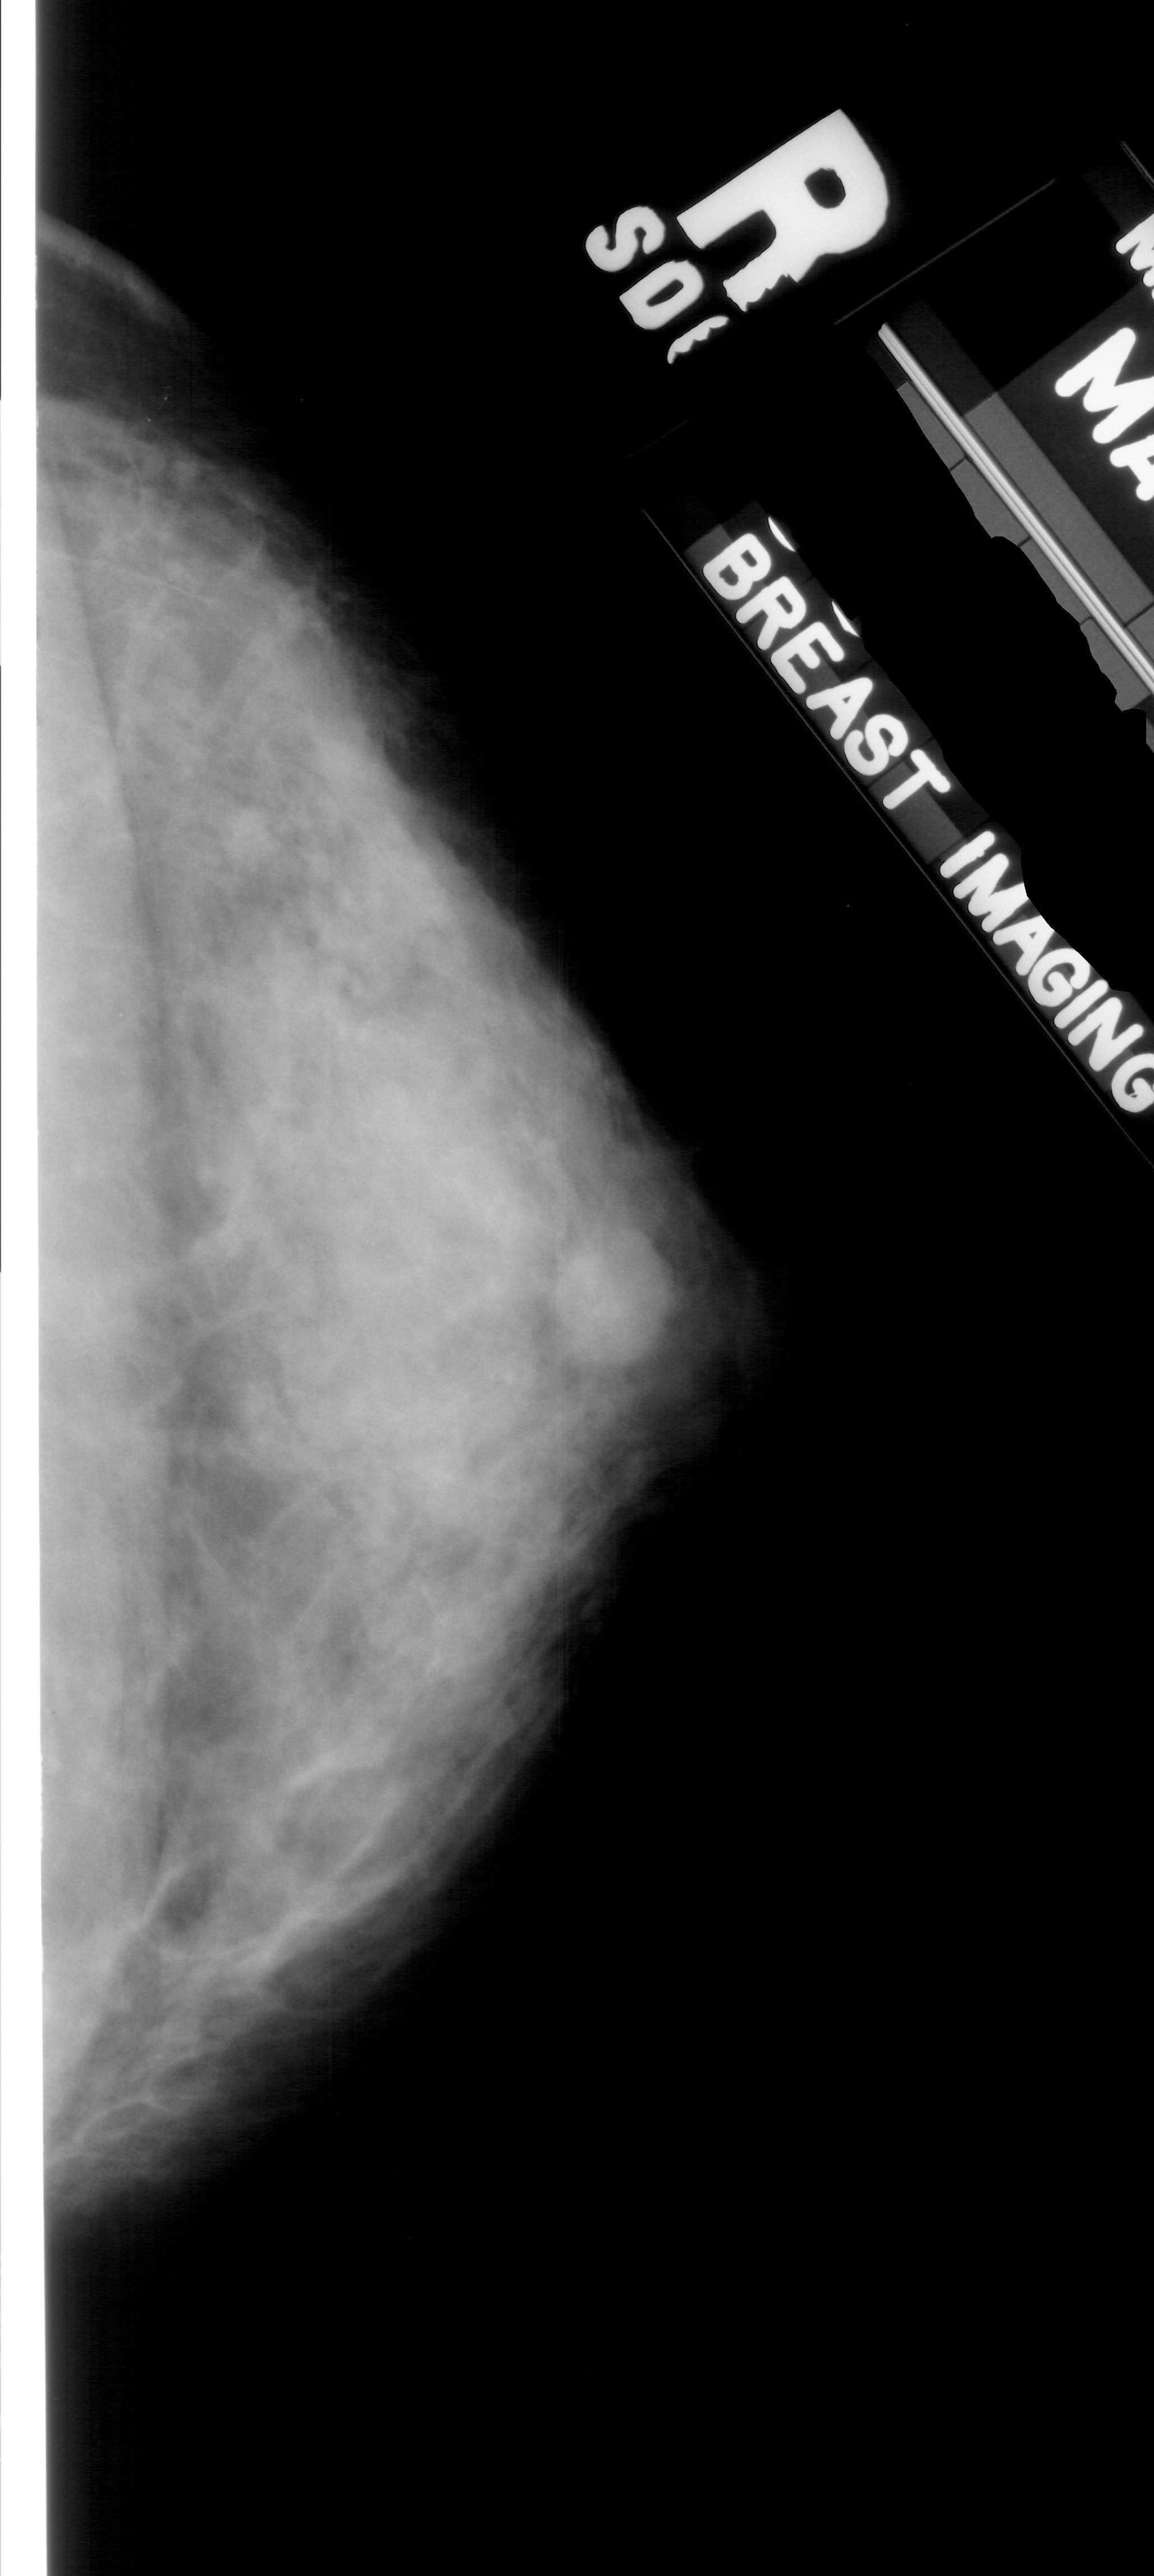
Scanned film-screen mammogram, right breast, craniocaudal (CC) view, breast composition: extremely dense (BI-RADS density category 4 of 4).
- Abnormality record for this image: mass, shape lobulated, margins microlobulated; BI-RADS assessment category 4; pathology result (as recorded, not read from the image): benign.